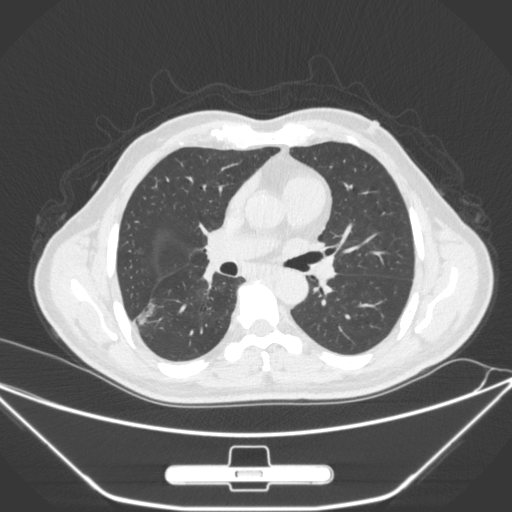
Chest CT, one axial slice; slice 158 of 310 in the series (ordered by position); 120 kVp; lung window (W 1500 / L -600 HU); 1 mm slice thickness; 512 × 512 image matrix, field of view 398 × 398 mm. Patient: male, 71 years. Case-level facts recorded for this patient, not image findings: clinical TNM (as recorded): T1c N0 M0; histopathological grade: G2.
Annotated regions visible in this slice (bounding box drawn by a radiologist):
- lung tumour (recorded histology: adenocarcinoma): bounding box <133,296,160,330> (left, top, right, bottom; pixels)